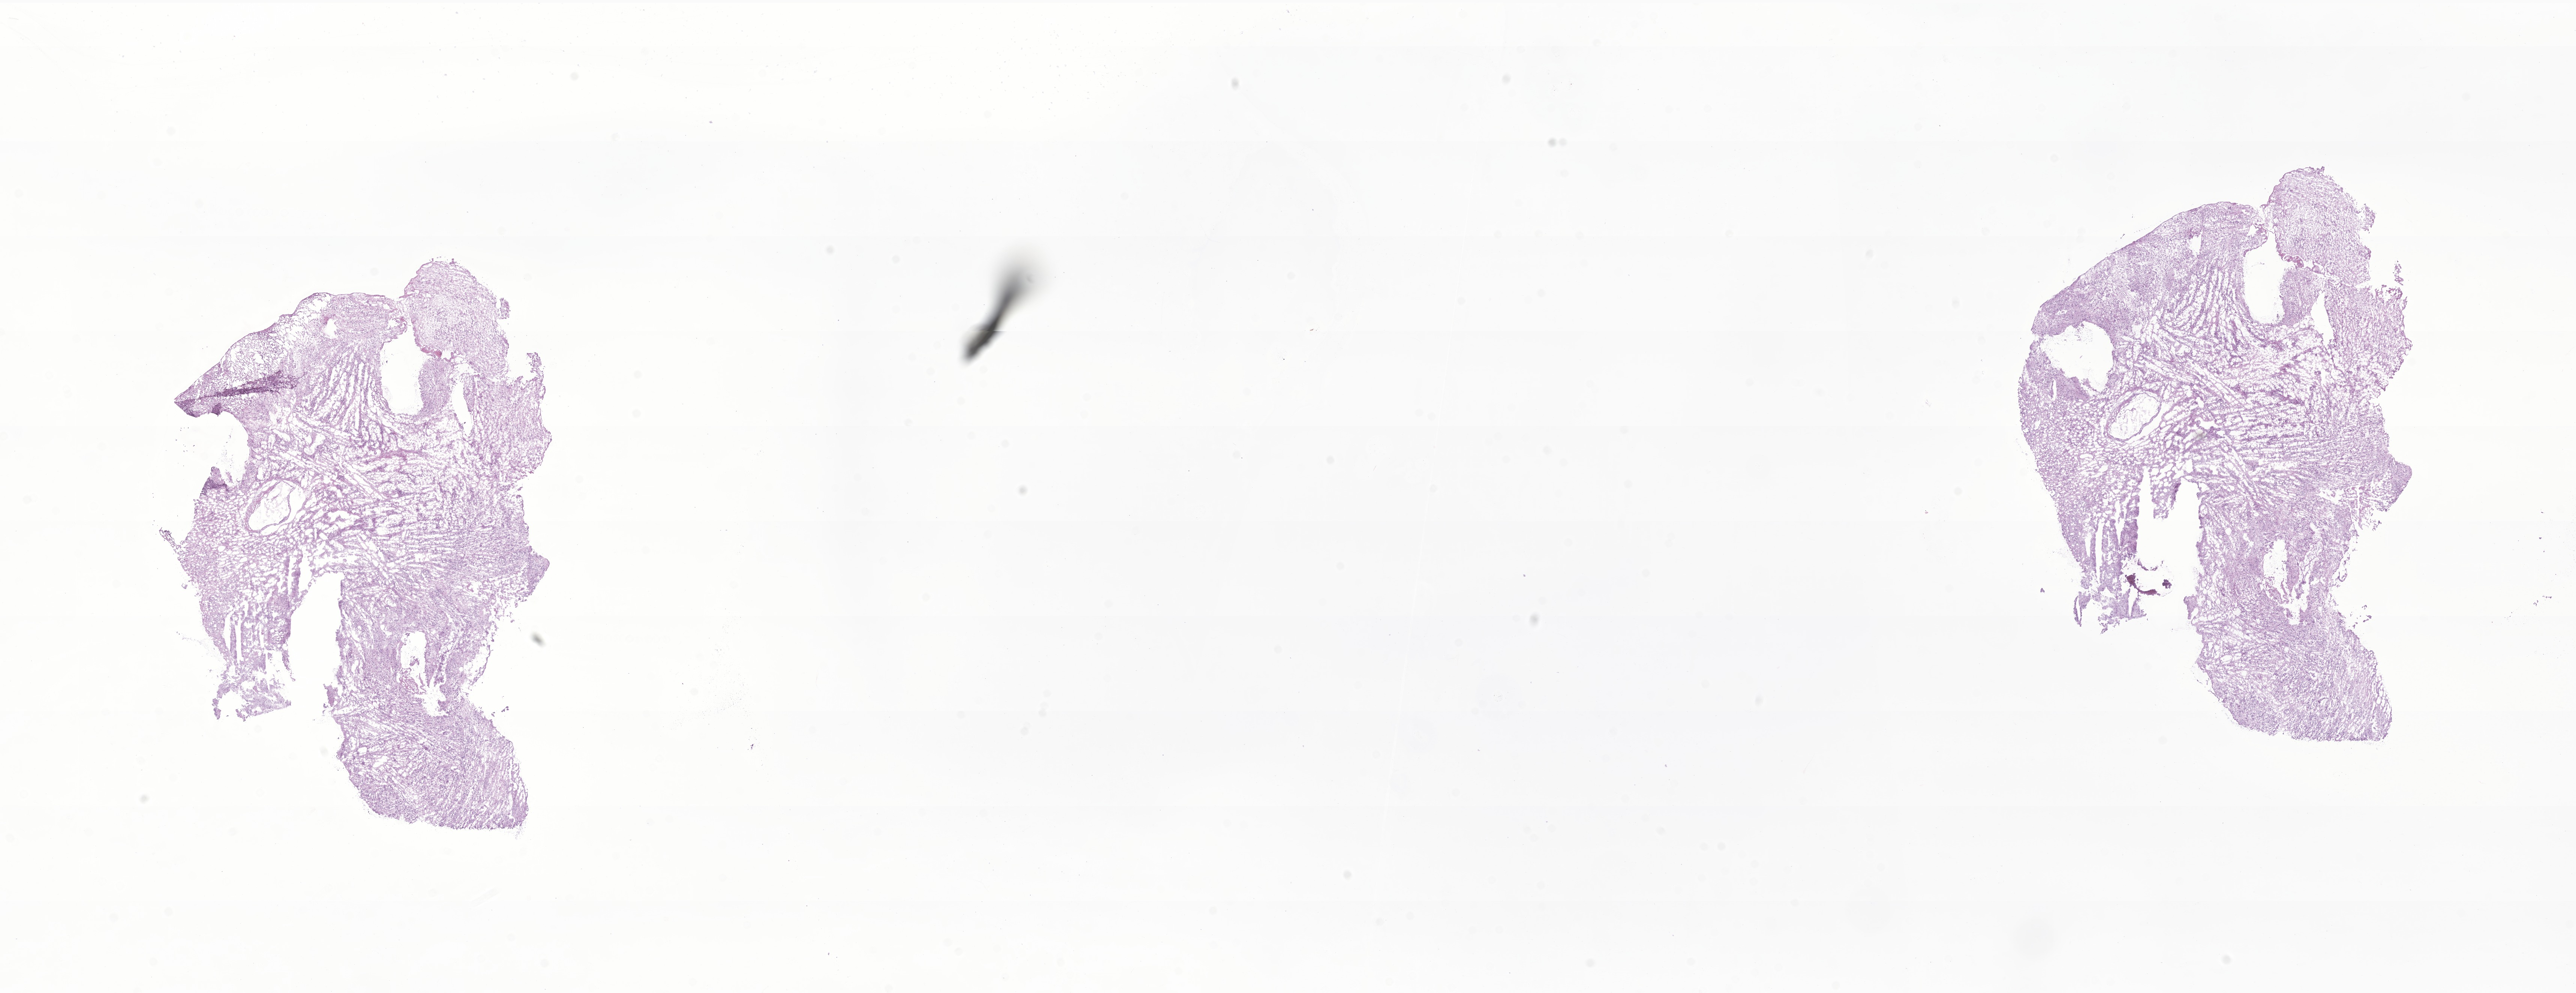
Digitized H&E-stained section of tumor tissue from the cerebral ventricle — shown as a low-resolution overview of the whole scanned area (about 29.0 x 11.2 mm), frozen section. Patient: male, age 82 months (6 years 10 months).
Diagnosis: Ependymoma, NOS.